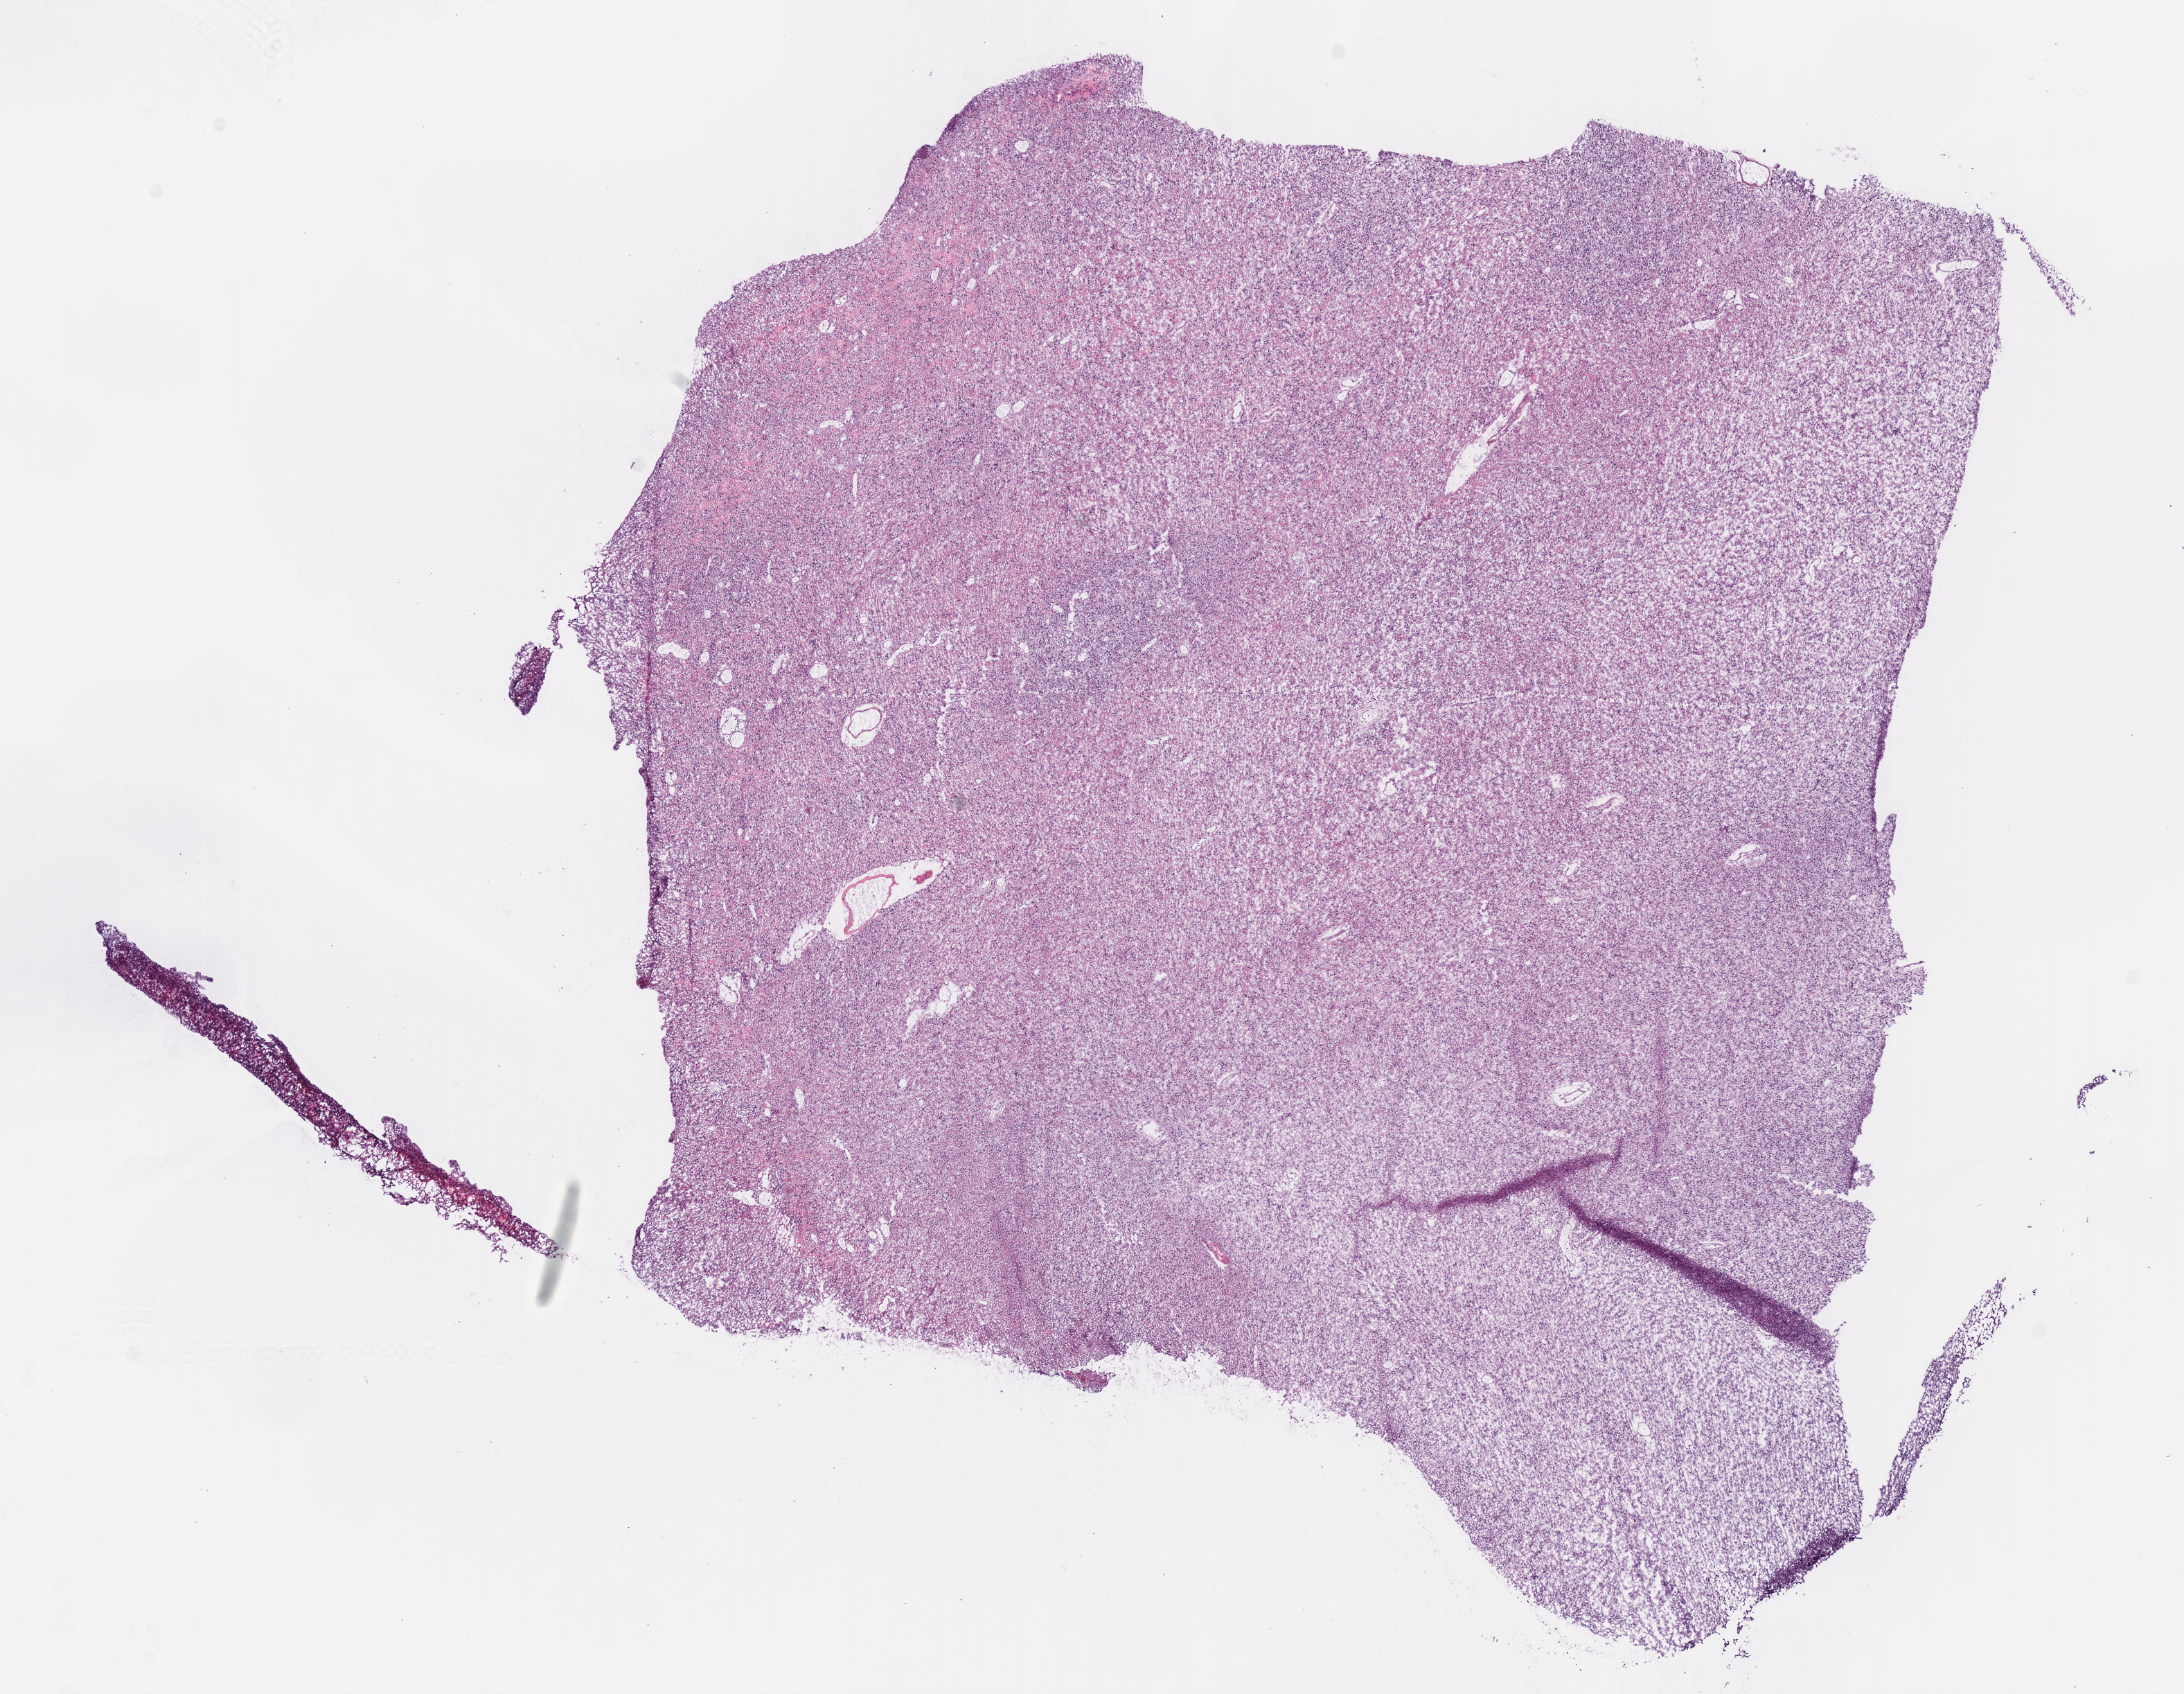
Whole-slide histology image, Hematoxylin and eosin (H&E) stained, shown as a low-resolution overview of the whole scanned area (about 12.4 x 9.6 mm); frozen section from the bottom of the tissue portion; brain, primary tumour sample. Patient: male, age at initial diagnosis 53 years. Histologic grade: G3 (poorly differentiated). Slide review estimates, as recorded: tumour cells 100%, tumour nuclei 85%, normal cells 0%, stromal cells 0%, necrosis 0%.
• pathologic diagnosis: Oligodendroglioma, anaplastic (cerebrum)
• laterality: left